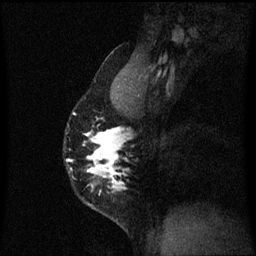
Breast MRI (dynamic contrast-enhanced), one sagittal slice. Slice 41 of 60 in the series (ordered by position). Dynamic contrast-enhanced series, image 2 of 3 at this slice position (ordered by acquisition). 1.5 T. TE 4.2 ms, TR 8.4 ms. 256 × 256 image matrix, field of view 200 × 200 mm. Female patient, age 40 years.
Outlined on this slice (semi-automatically segmented with operator editing):
- analysis volume of interest (the breast-tissue region the enhancement analysis was run in; not a lesion): bounding box <66,104,123,211> (left, top, right, bottom; pixels)
- tumour enhancement mask (voxels above the 70 % enhancement threshold inside the analysis volume of interest): <72,112,123,193>